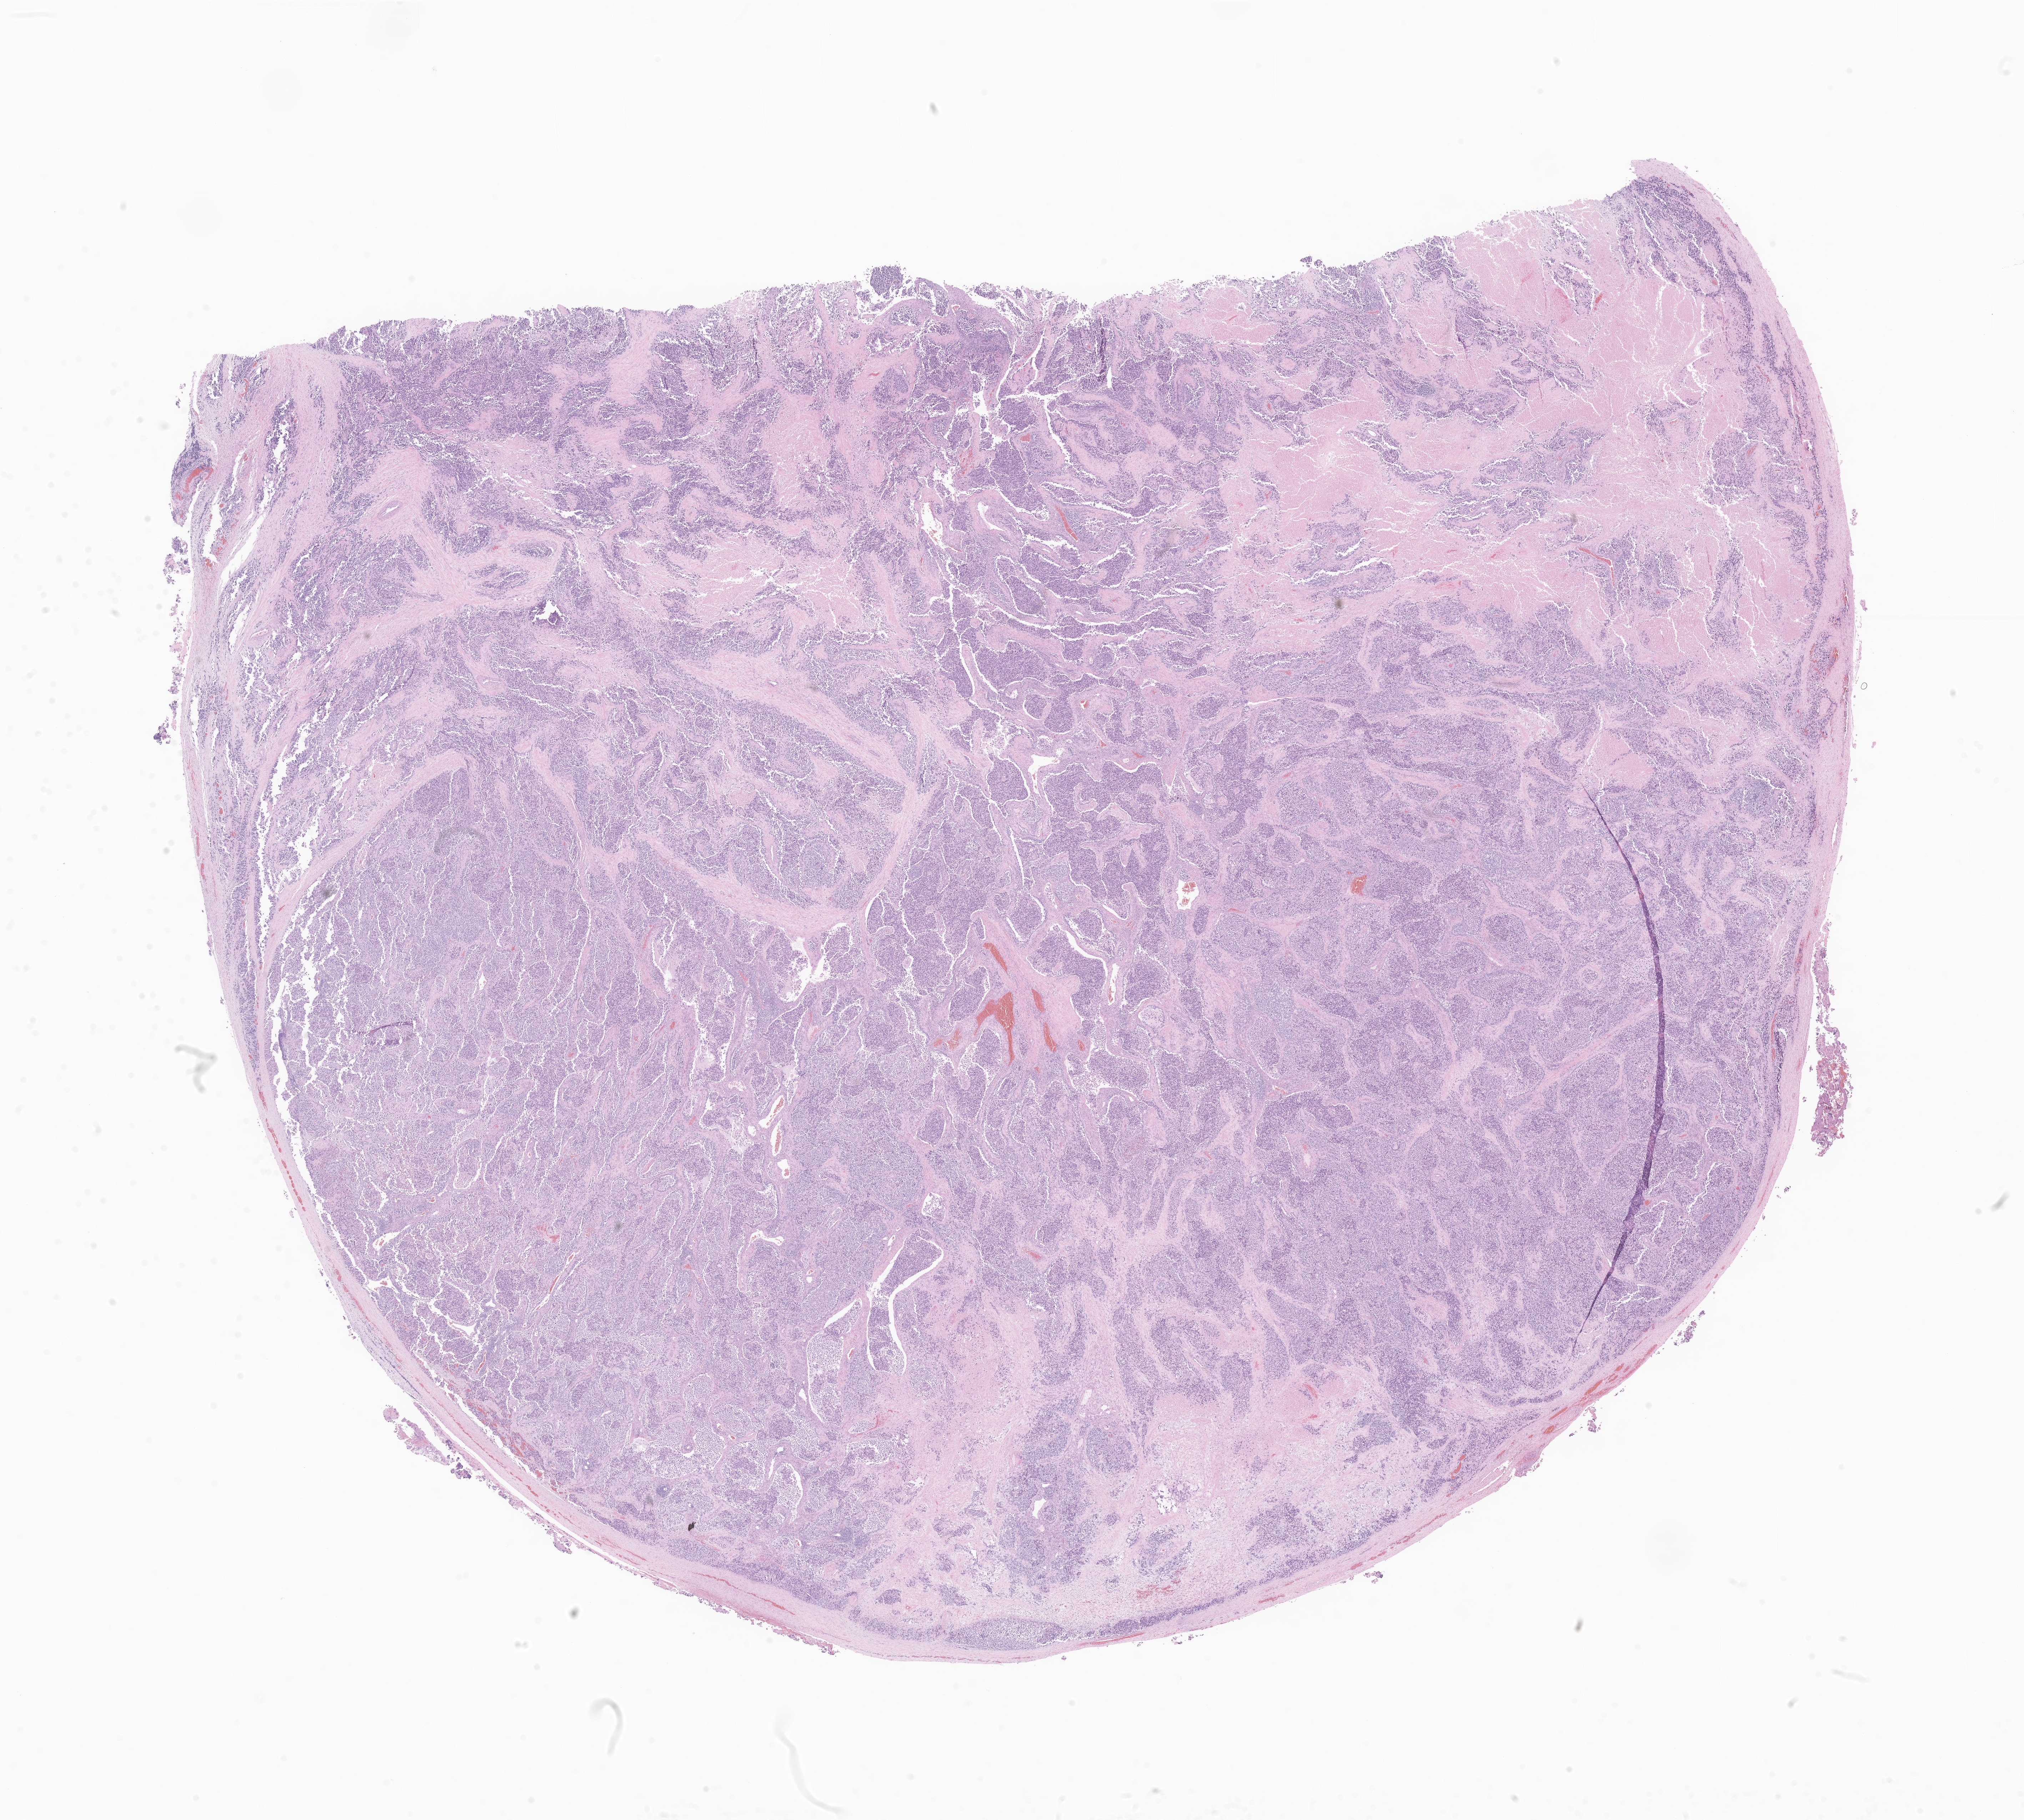
Whole-slide image, hematoxylin and eosin (H&E) stain of tumor tissue from the soft tissue of thorax, shown as a low-resolution overview of the whole scanned area (about 23.9 x 21.5 mm); FFPE section. Male patient, age 169 months (14 years 1 month).
• diagnosis (ICD-O-3 morphology term): Alveolar rhabdomyosarcoma